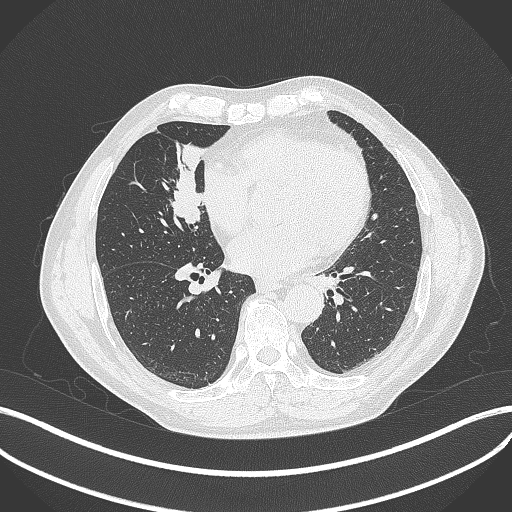
Chest CT, one axial slice; position 168 of 429 along the scan axis; 120 kVp; lung window (W 1500 / L -600 HU); 1 mm slice thickness; 512 × 512 image matrix, field of view 400 × 400 mm. Male patient, age 61 years. Case-level facts recorded for this patient, not image findings: clinical TNM (as recorded): T2b N1 M0.
Structures marked on this image (rectangle marked by the reading radiologist):
- lung tumour (recorded histology: squamous cell carcinoma): bounding box [x1, y1, x2, y2] px = [169, 161, 213, 232]